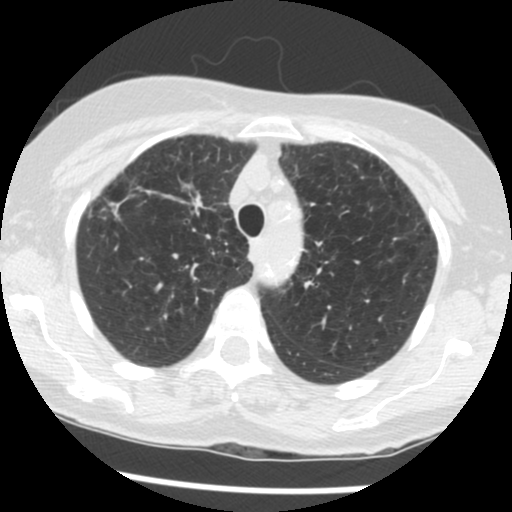
Chest CT (low-dose screening protocol), one axial image, second screening round (one year after baseline), lung window (W 1500 / L -600 HU), standard (soft-tissue) reconstruction kernel (STANDARD), 120 kVp, slice 28 of 124 in the series. Female participant, aged 70 years at enrolment. Former smoker at enrolment.
Lesion marked by an expert reader, box from (x=155, y=165) to (x=227, y=223) px. Screening reader's record for this exam (one nodule recorded; not confirmed to be the boxed lesion): non-calcified nodule or mass ≥4 mm, right upper lobe, 11 × 7 mm, spiculated (stellate) margins, soft tissue attenuation, pre-existing on the prior screen: yes; interval growth: yes. Later outcome: lung cancer diagnosed 248 days after this screen — non-small cell carcinoma, right upper lobe, stage IV (AJCC 6th edition), 30 mm at pathology.